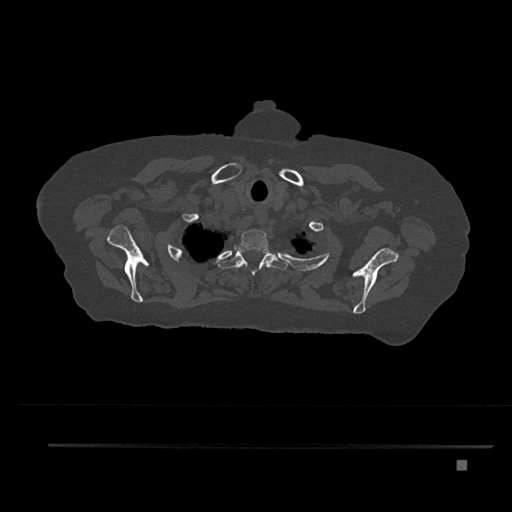
CT including the spine, one axial slice. Slice 679 of 797 in the series (ordered by position). Reconstruction kernel Br40s/3. 120 kVp. Bone window (W 1800 / L 400 HU). 0.5 mm slice thickness. 512 × 512 image matrix. Patient: female, 76 years. Case-level facts recorded for this patient, not image findings: primary cancer: lung.
Structures marked on this image (semi-automatic segmentation, software-assisted and operator-edited):
- T1 vertebra: bounding box [x1, y1, x2, y2] px = [240, 229, 268, 251]
- T2 vertebra: [218, 247, 289, 276]